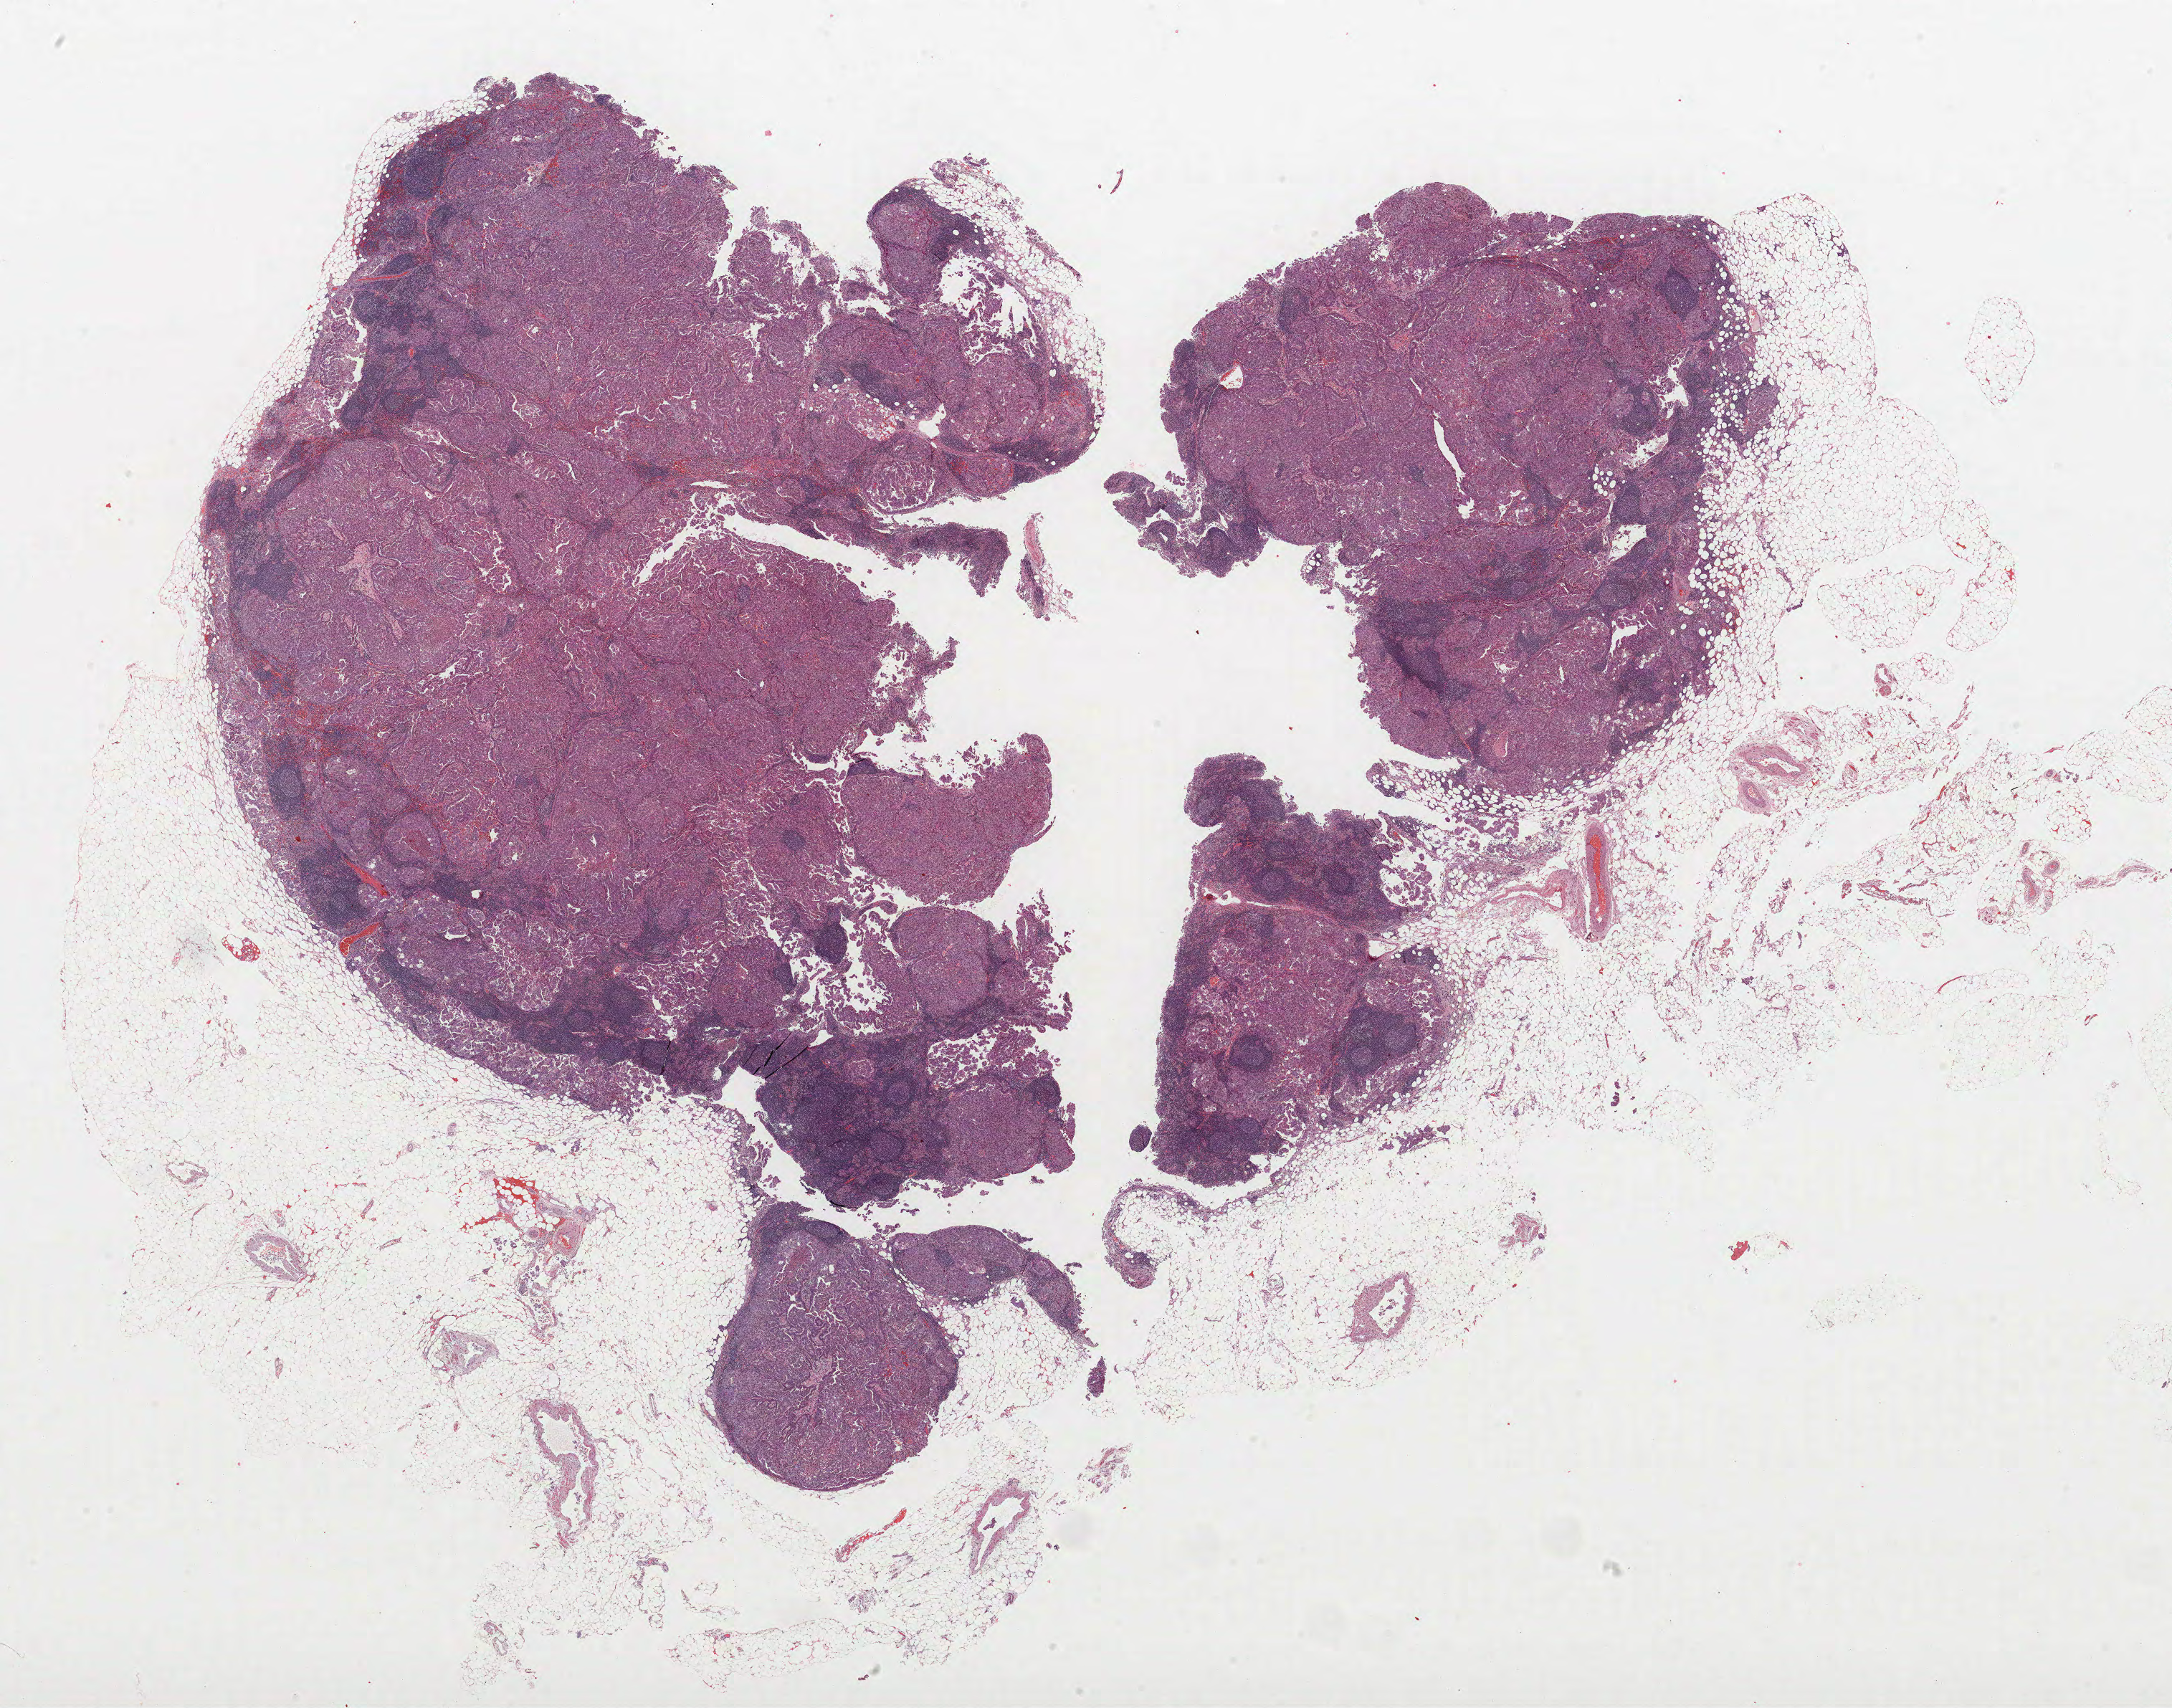
H&E whole-slide image, a low-resolution overview of the entire scanned area, about 24.2 x 19.1 mm (acquisition: 40x scan), formalin-fixed paraffin-embedded (FFPE) section, lung. Male, age 74 at enrolment. Grade: cannot be assessed (GX).
Stage (AJCC 6th edition): IIIA. Primary tumour location (clinical record): left upper lobe. ICD-O-3 topography: upper lobe of lung (C34.1). Tumour size (pathology): 40 mm. Participant's lung-cancer diagnosis: Adenocarcinoma, NOS.